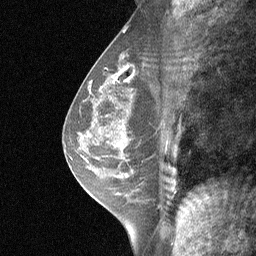
Breast MRI (dynamic contrast-enhanced), one sagittal slice; dynamic contrast-enhanced study with each time point stored as its own series, time point 2 of 3 at this slice position (early post-contrast, ordered by acquisition time); 1.5 T; TE 4.8 ms, TR 27 ms; 2 mm slice thickness; 256 × 256 image matrix, field of view 180 × 180 mm. Female patient, age 47 years. Case-level facts recorded for this patient, not image findings: setting: breast cancer imaged before/during neoadjuvant chemotherapy; receptor status: HR-positive, HER2-negative.
Annotated regions visible in this slice (semi-automatically segmented with operator editing):
- analysis volume of interest (the breast-tissue region the enhancement analysis was run in; not a lesion): bounding box [x1, y1, x2, y2] px = [104, 138, 165, 198]
- tumour enhancement mask (voxels above the 90 % enhancement threshold inside the analysis volume of interest): [118, 143, 121, 146]